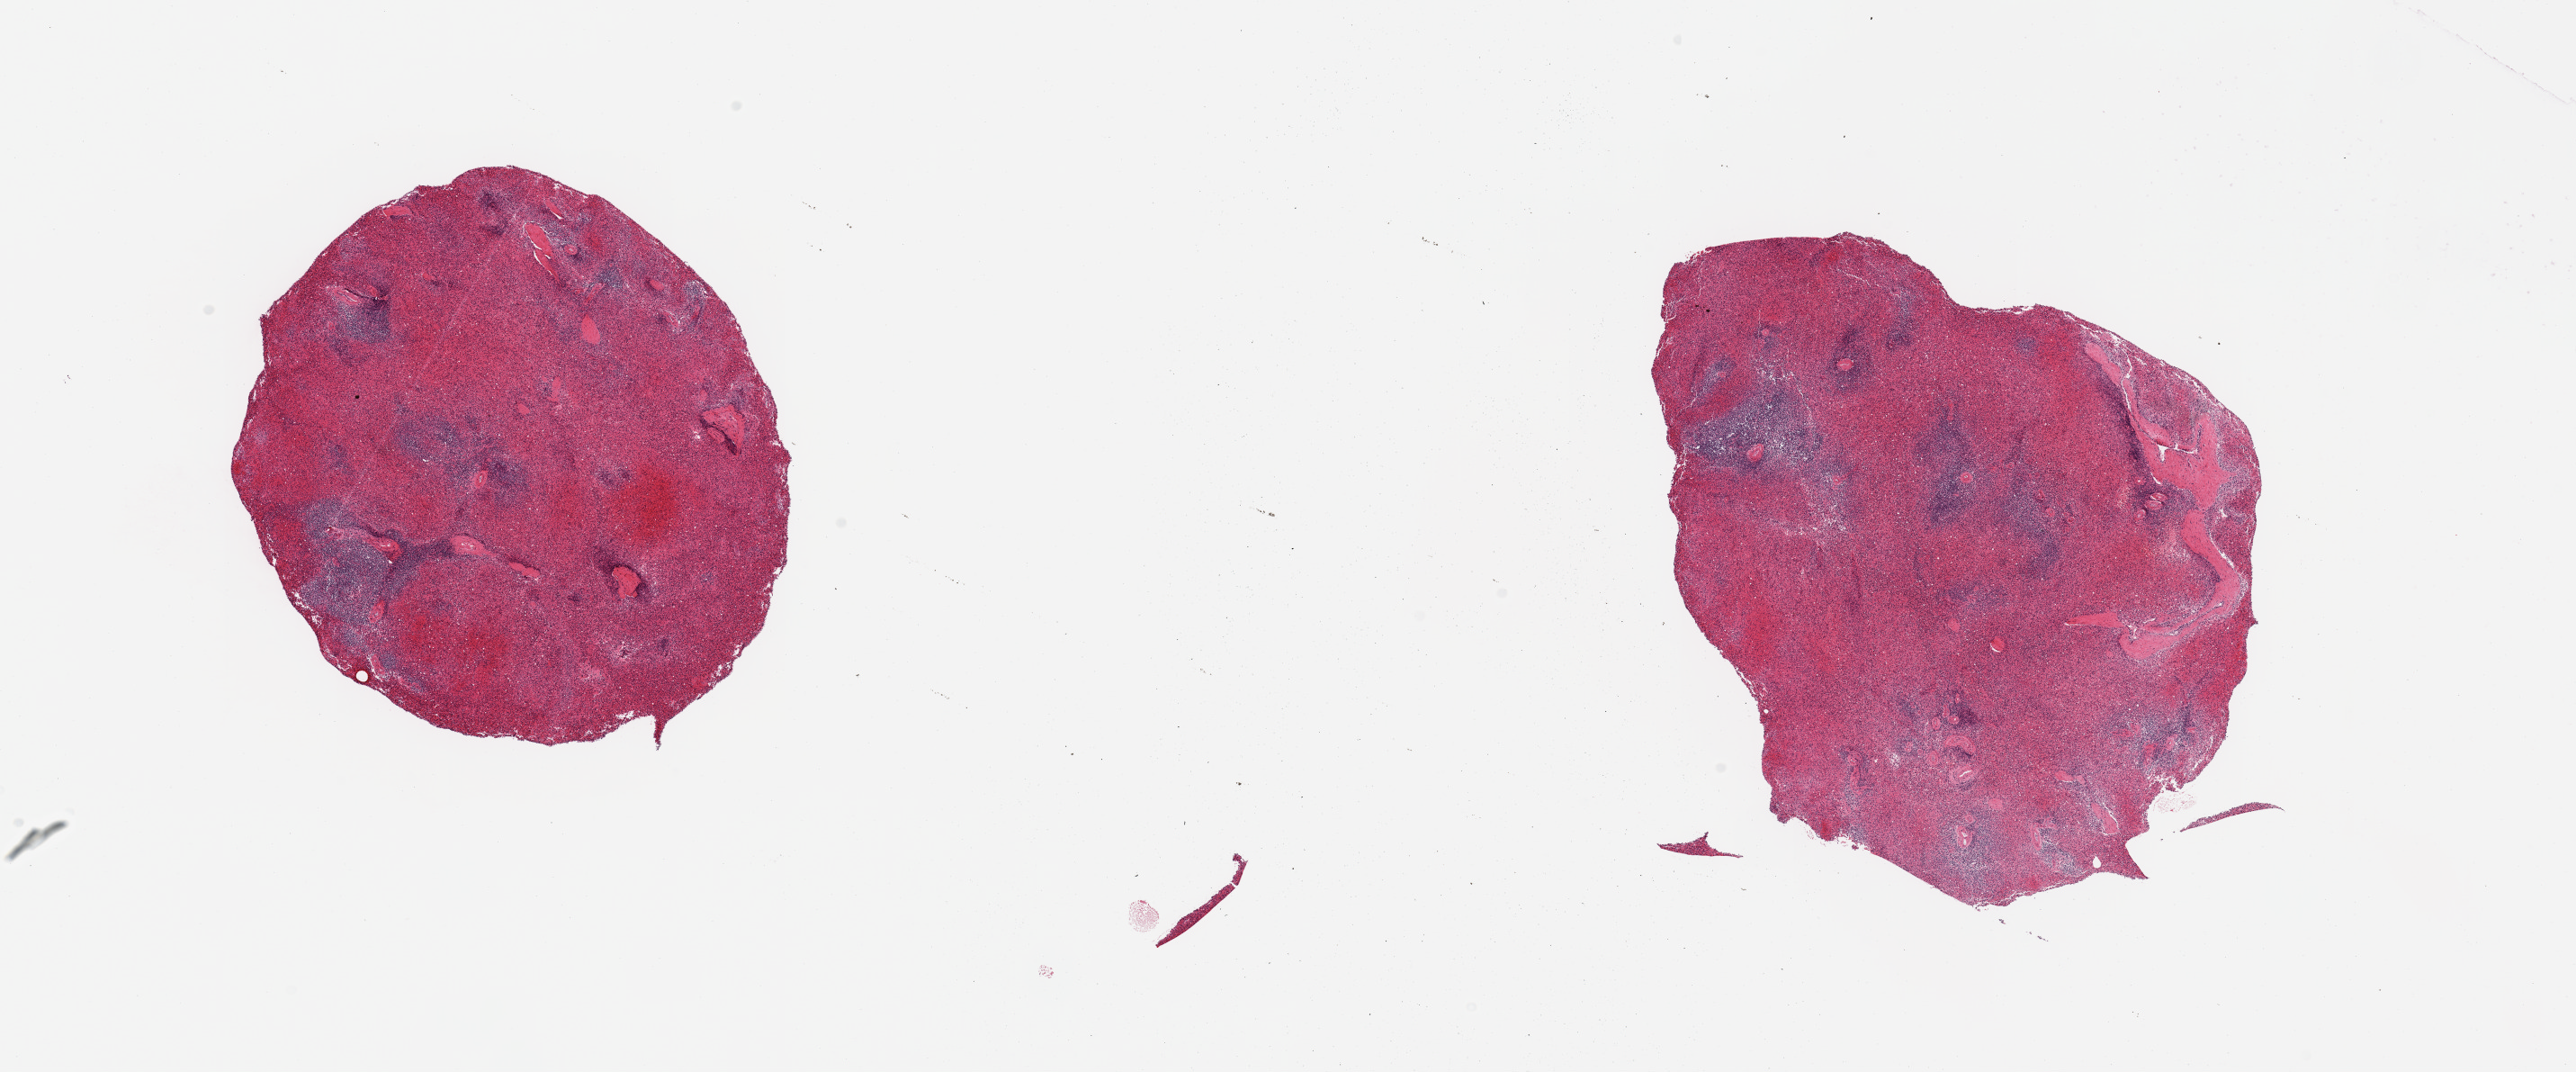
H&E whole-slide image, brightfield, low-resolution overview of the scanned area, about 22.6 x 9.4 mm; PAXgene-fixed paraffin-embedded (PFPE) section; sampled site (target tissue): spleen; tissue donor sample.
• pathologist's review note for this sample: 2 pieces